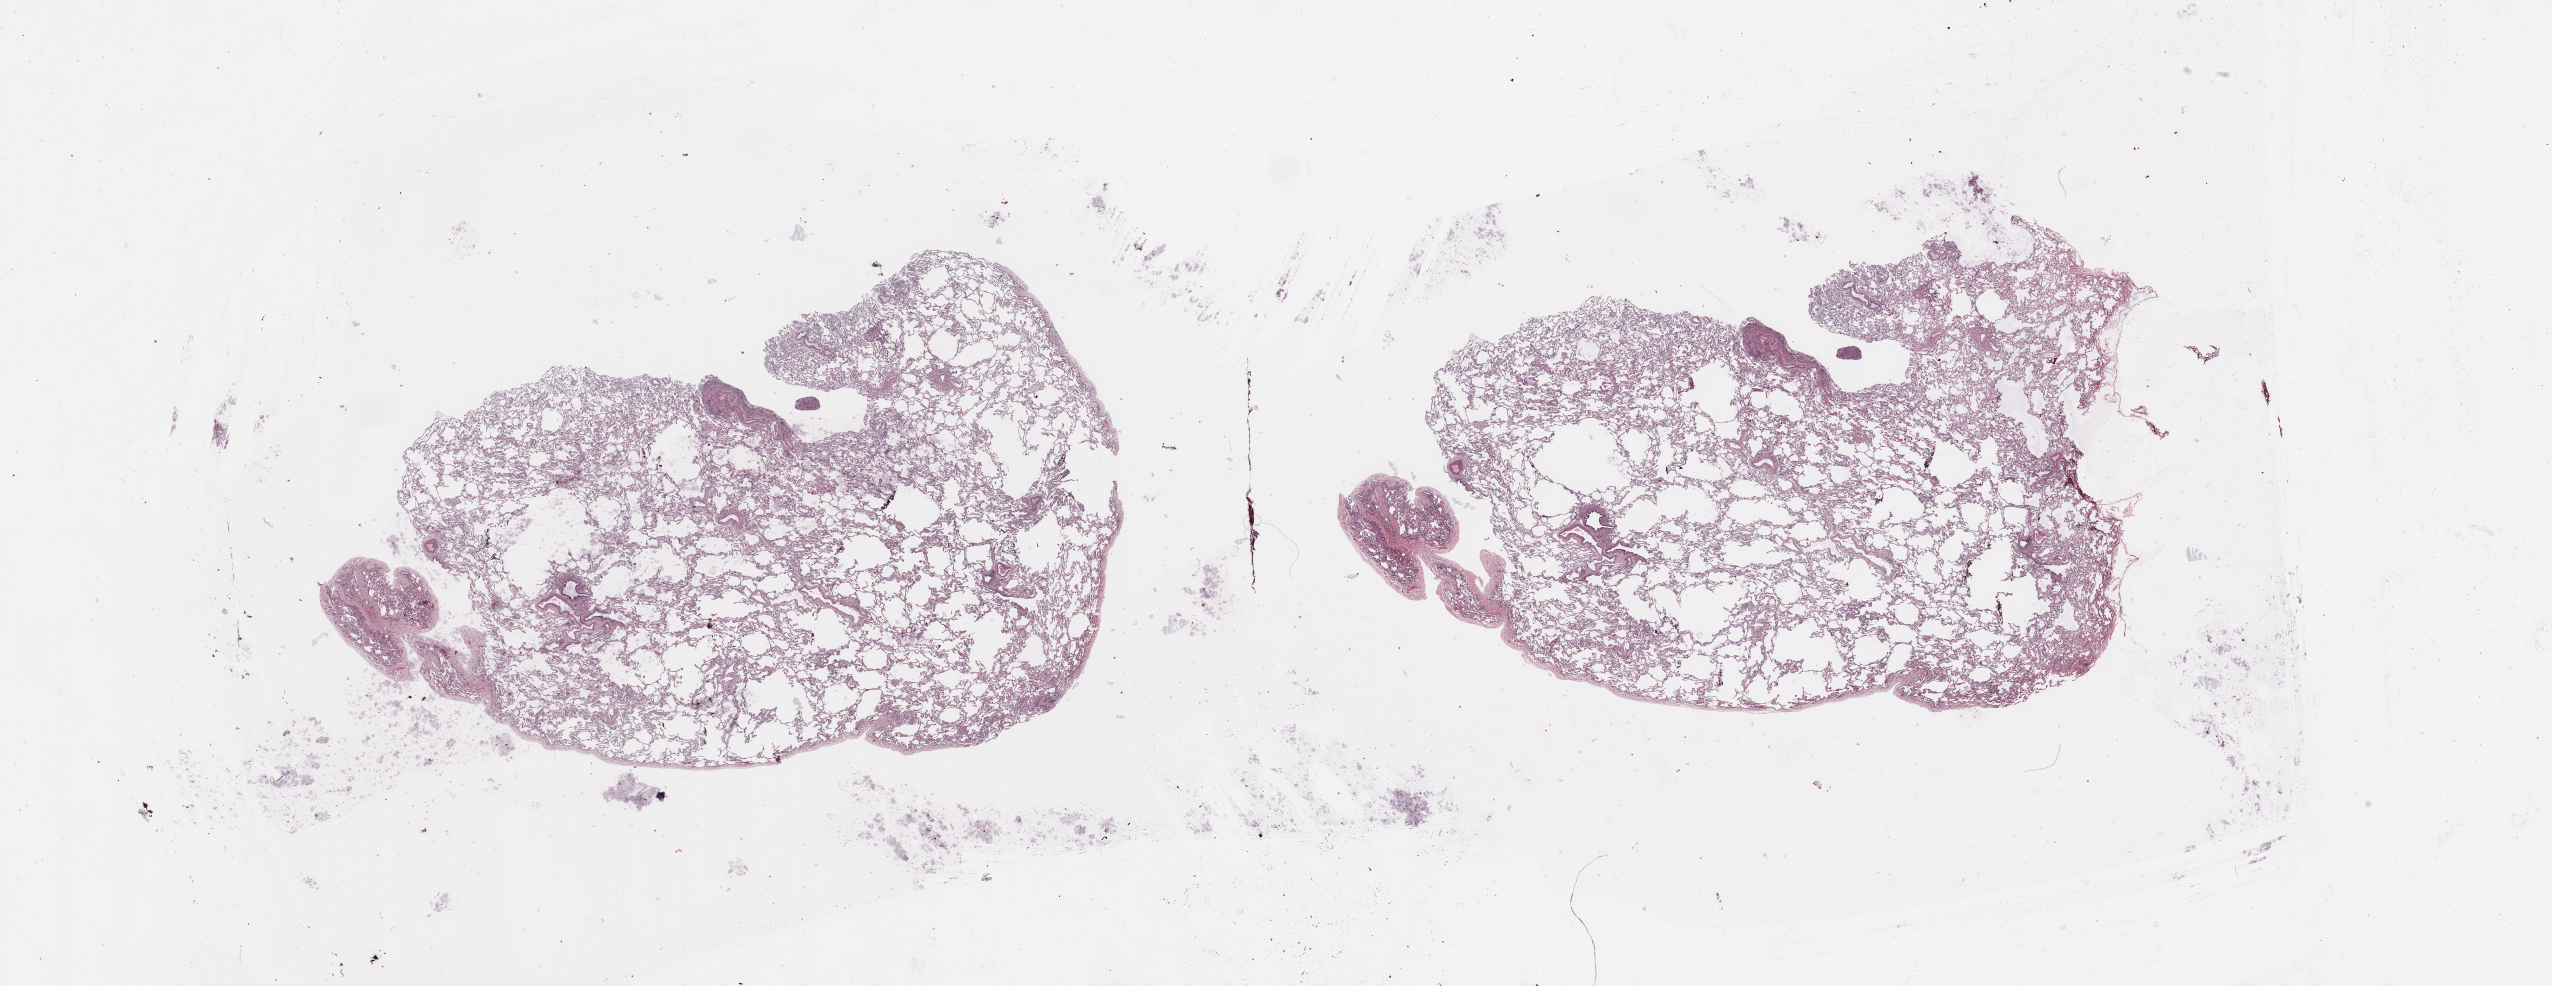
Whole-slide histology image, H&E-stained — whole scanned area (about 40.4 x 15.6 mm, slide scanned at 20x) shown as a low-resolution overview, normal (non-tumour) tissue sample, lung. Female, 61 y/o.
This section: normal (non-tumour) tissue from the same patient. Patient diagnosis: Adenocarcinoma, NOS.